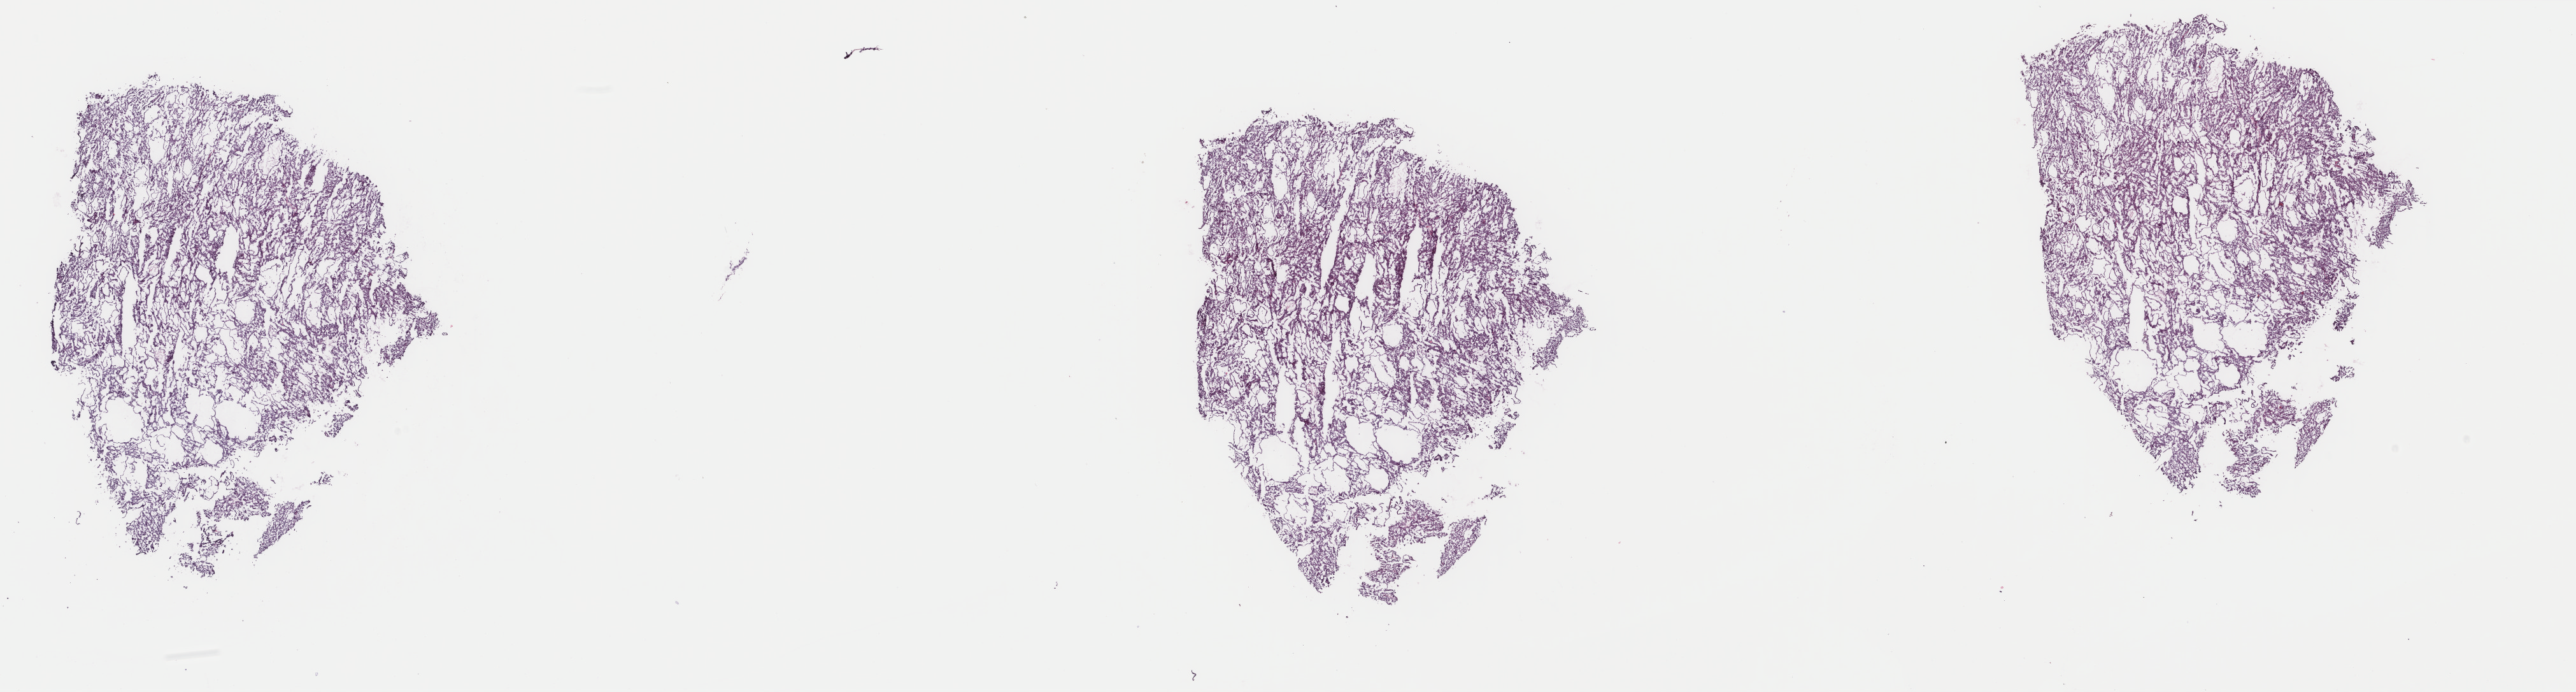
Whole-slide histology image, Hematoxylin and eosin (H&E) stained, whole scanned area (about 32.1 x 8.6 mm) shown as a low-resolution overview, frozen section from the top of the tissue portion, kidney, primary tumour sample. Patient: male, age at initial diagnosis 66 years. Composition of this section per pathologist review: tumour cells 100%, tumour nuclei 80%, normal cells 0%, stromal cells 0%, necrosis 0%. Inflammatory infiltration, as recorded: lymphocyte infiltration 1%, monocyte infiltration 1%, neutrophil infiltration 0%.
AJCC pathologic stage: I (7th edition). Pathologic diagnosis: Papillary adenocarcinoma, NOS. TNM: T1a NX MX. Laterality: left.